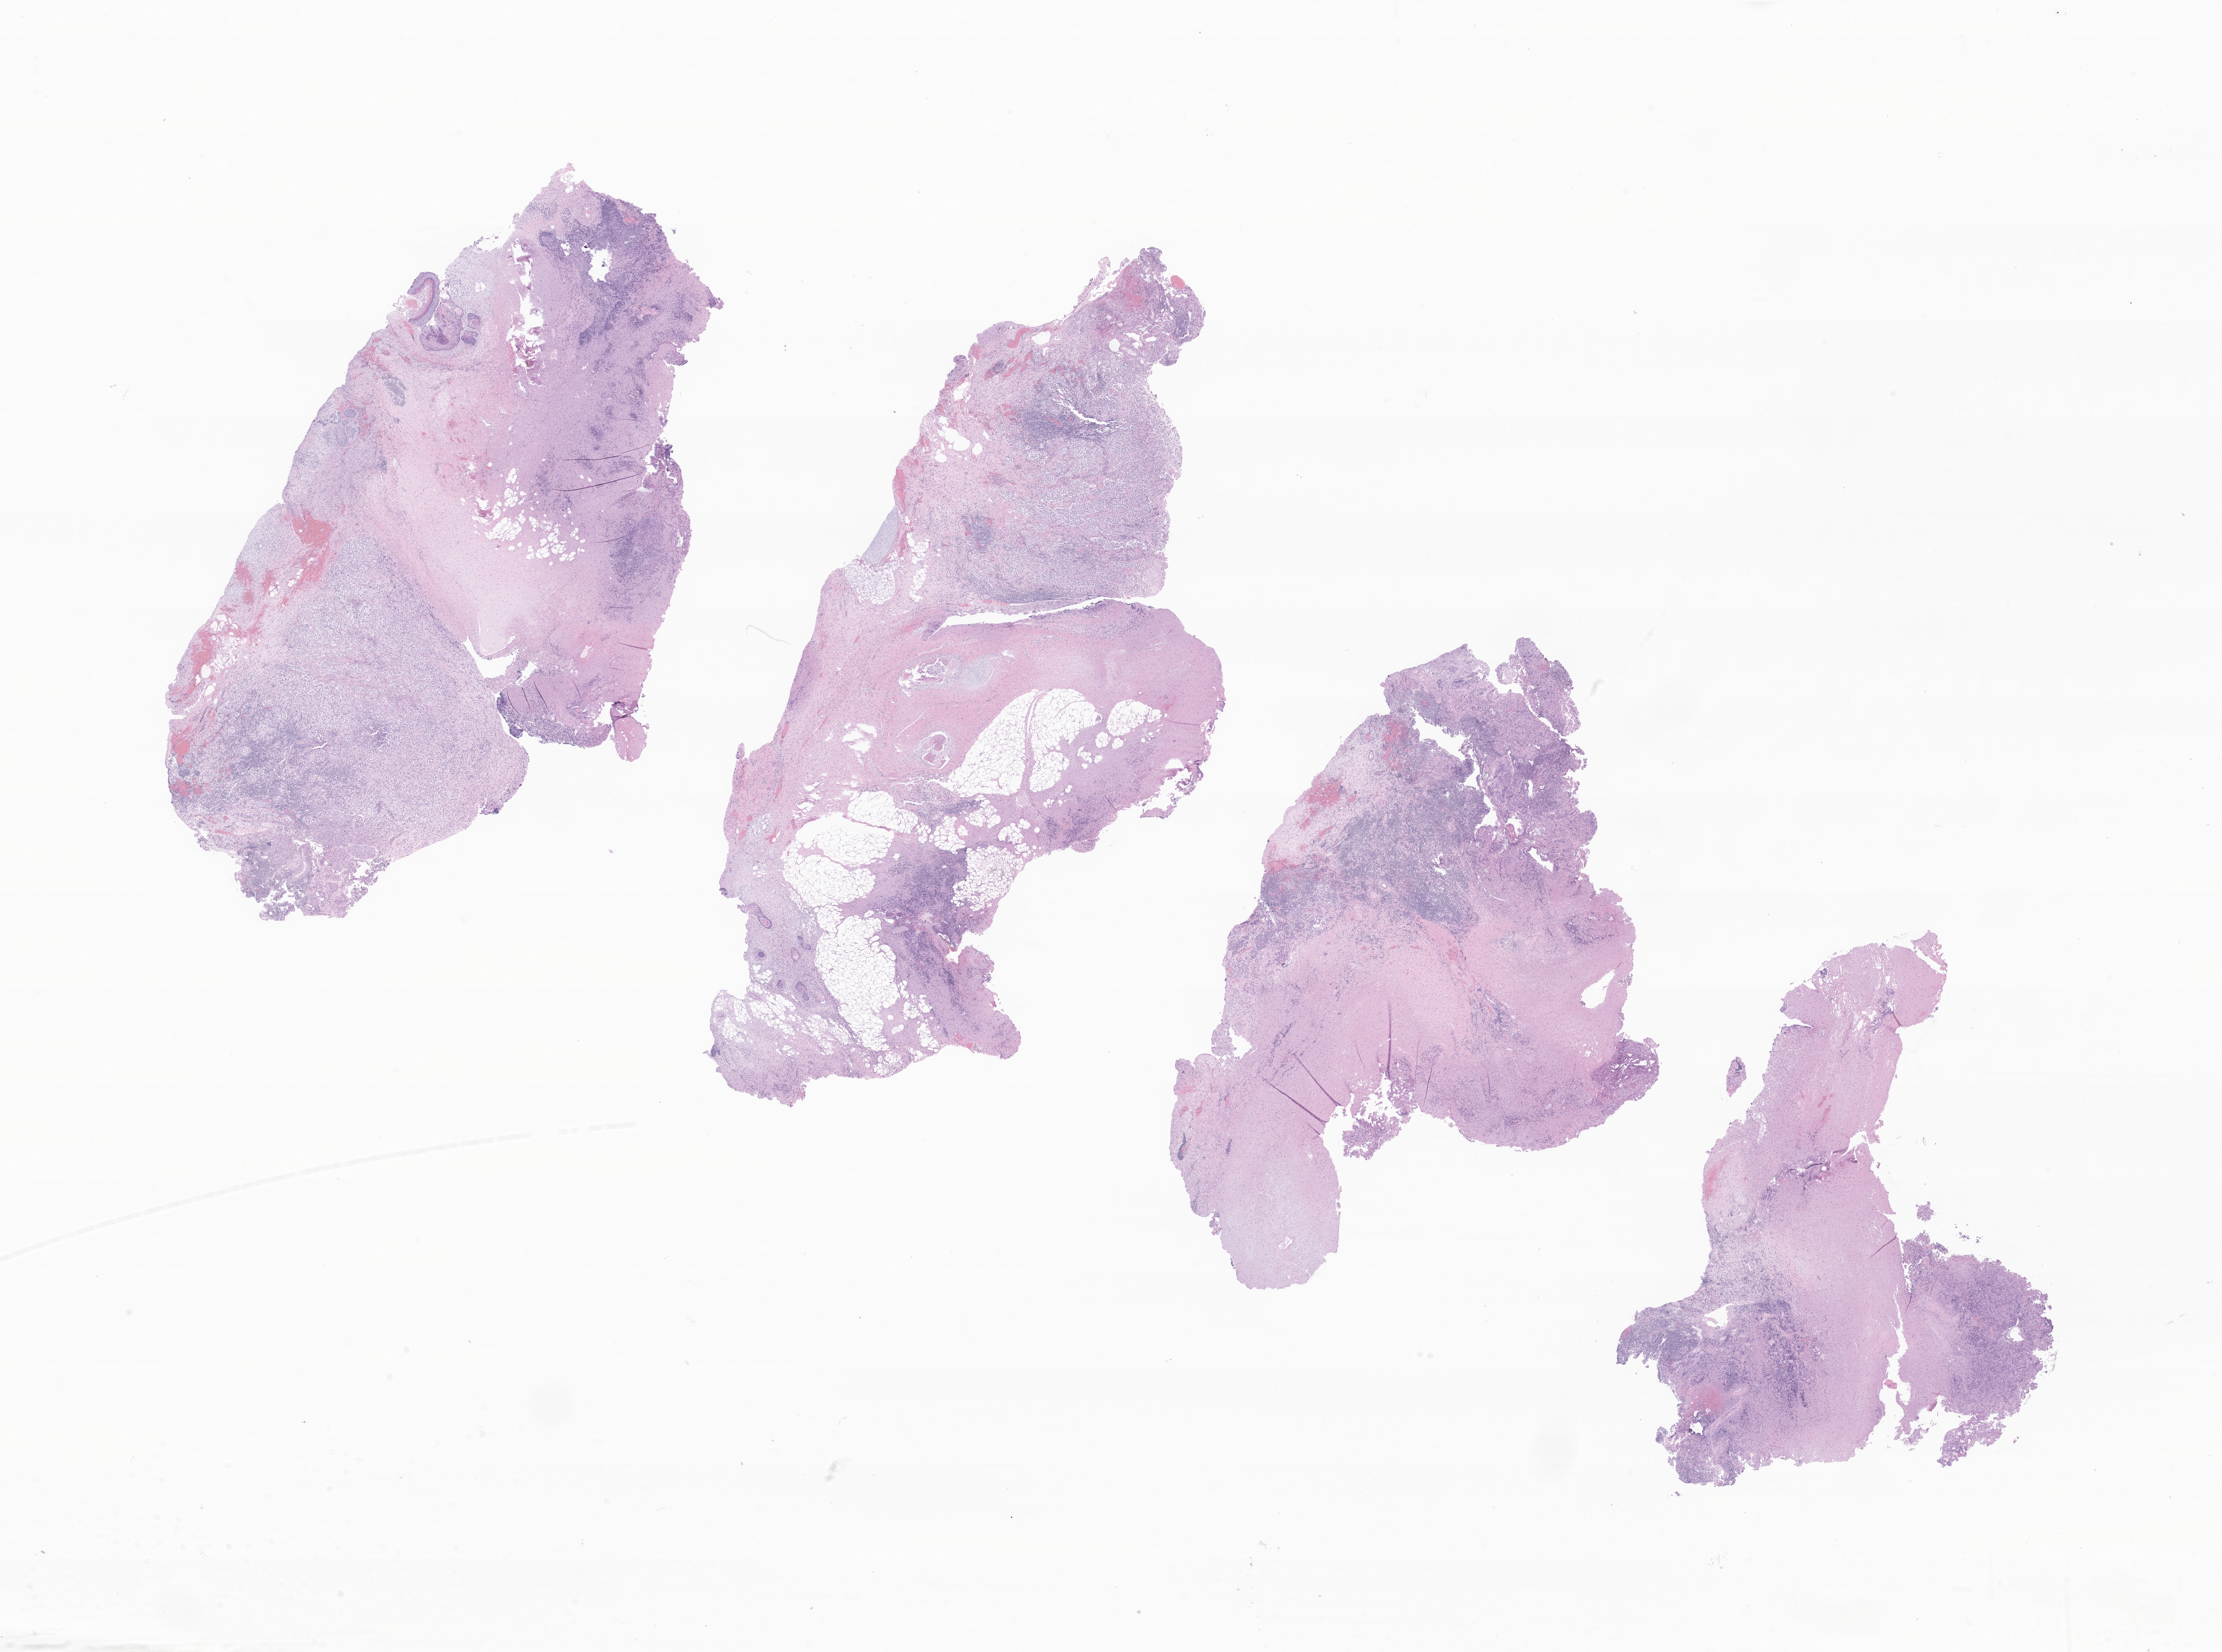
H&E whole-slide image of tumor tissue from the brain, a low-resolution overview of the entire scanned area, about 24.9 x 18.5 mm; formalin-fixed, paraffin-embedded (FFPE) tissue. Male patient, age 244 months (20 years 4 months).
Diagnosis (ICD-O-3 morphology term): Mixed germ cell tumor.